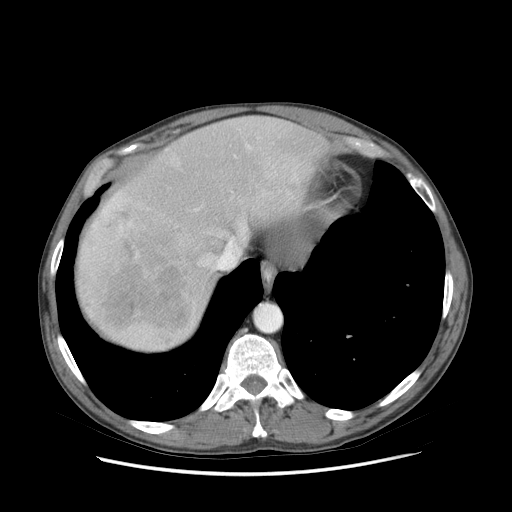
Contrast-enhanced abdominal CT (liver protocol), one axial slice. Slice 67 of 89 in the series (ordered by position). Reconstruction kernel STANDARD. Soft-tissue window (W 400 / L 40 HU). 2.5 mm slice thickness. 512 × 512 image matrix. From the clinical record (not read from this slice): diagnosis: hepatocellular carcinoma (patient treated with transarterial chemoembolisation; whether this scan precedes or follows treatment is not stated here); TNM stage (as recorded): Stage-IIIB; Child-Pugh class: A.
Outlined on this slice (semi-automatically segmented with operator editing):
- abdominal aorta: box from (x=256, y=305) to (x=280, y=331) px
- liver parenchyma outside the tumour (the mass and vessels are separate outlines, so this box may not span the whole liver): (x=78, y=116)–(x=330, y=350)
- mass: (x=92, y=209)–(x=191, y=333)
- liver vessels: (x=87, y=144)–(x=274, y=265)